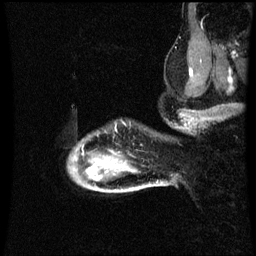
Breast MRI (dynamic contrast-enhanced), one sagittal slice; slice 54 of 60 in the series (ordered by position); dynamic contrast-enhanced series, image 2 of 3 at this slice position (ordered by acquisition); 1.5 T; TE 4.2 ms, TR 8.9 ms; 2 mm slice thickness; 256 × 256 image matrix, field of view 200 × 200 mm. Female patient, age 49 years. From the clinical record (not read from this slice): setting: breast cancer imaged before/during neoadjuvant chemotherapy; receptor status: HR-positive, HER2-negative.
Structures marked on this image (semi-automatic segmentation, software-assisted and operator-edited):
- analysis volume of interest (the breast-tissue region the enhancement analysis was run in; not a lesion): bounding box (x1, y1, x2, y2) in pixels: (70, 140, 159, 193)
- tumour enhancement mask (voxels above the 70 % enhancement threshold inside the analysis volume of interest): (88, 158, 121, 175)